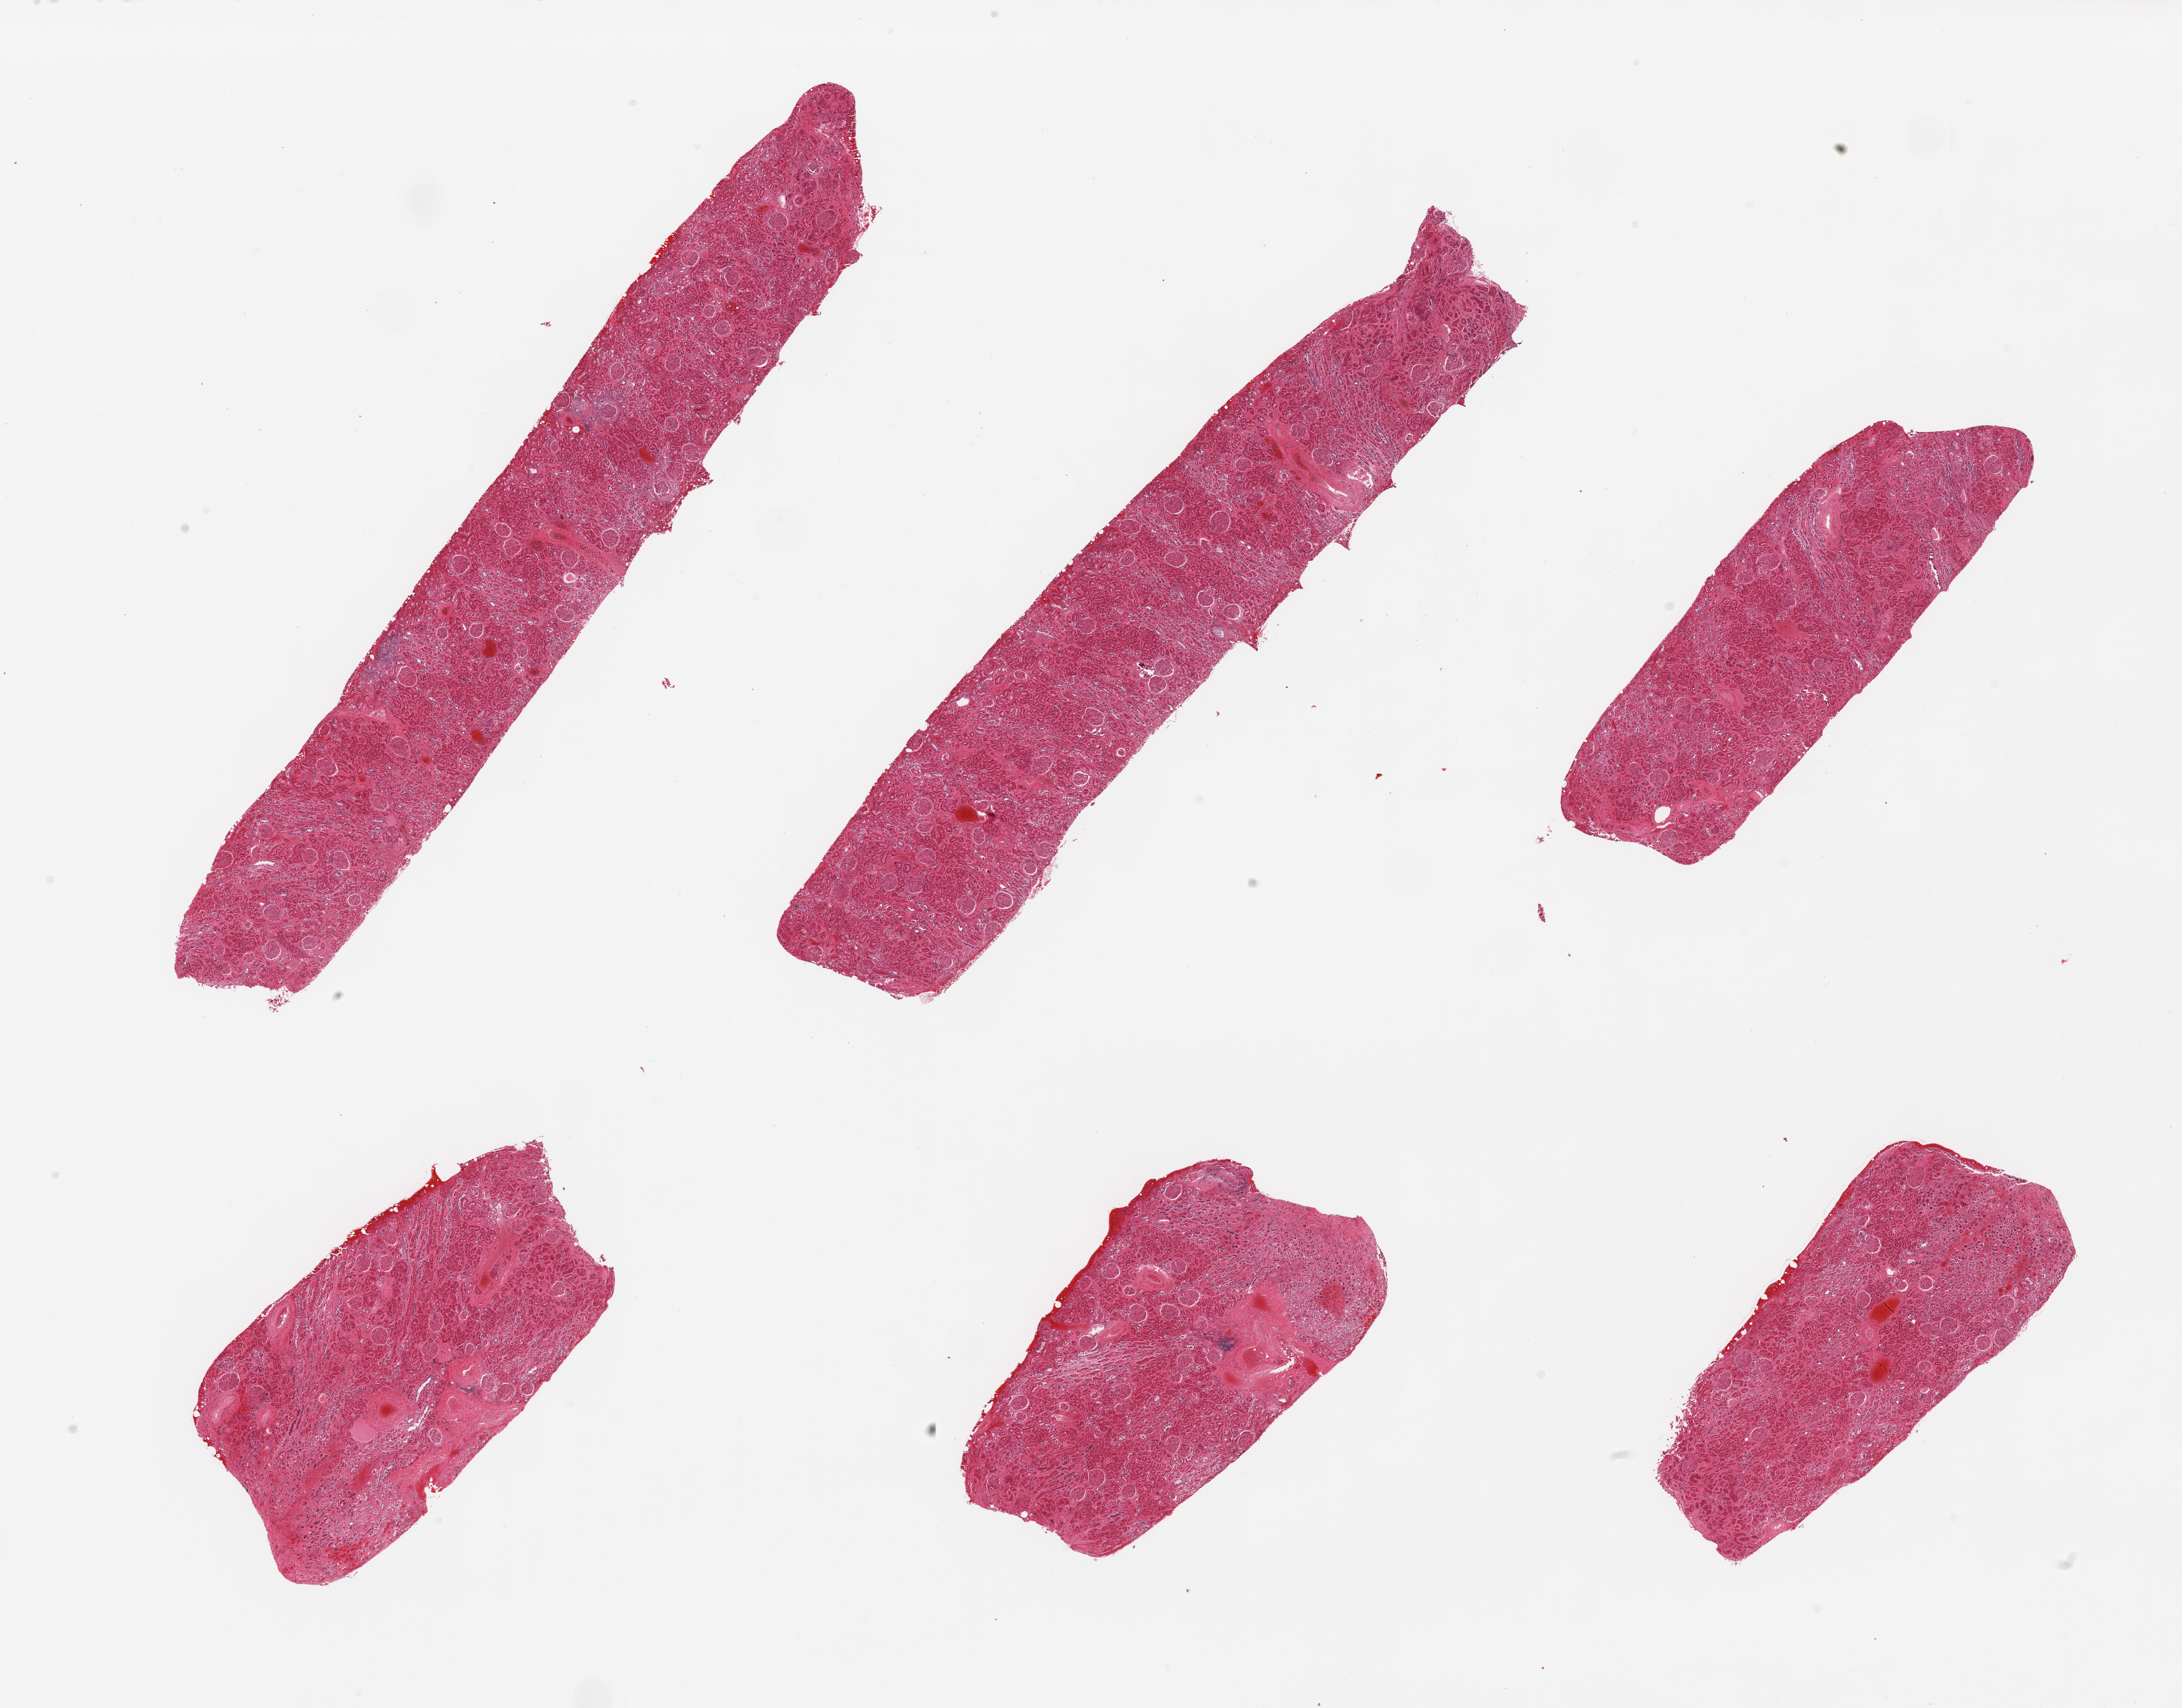
Haematoxylin and eosin whole-slide image — shown as a low-resolution overview of the whole scanned area (about 27.6 x 21.6 mm, from a 20x scan); PAXgene-fixed, paraffin-embedded tissue; section of renal cortex (target tissue); tissue donor sample. Male donor.
Review note (as recorded): 6 pieces; glomeruli in all sections, rare collections of lymphocytes, mild interstitial fibrosis, some vascular thickening, few sections include portion of medulla.